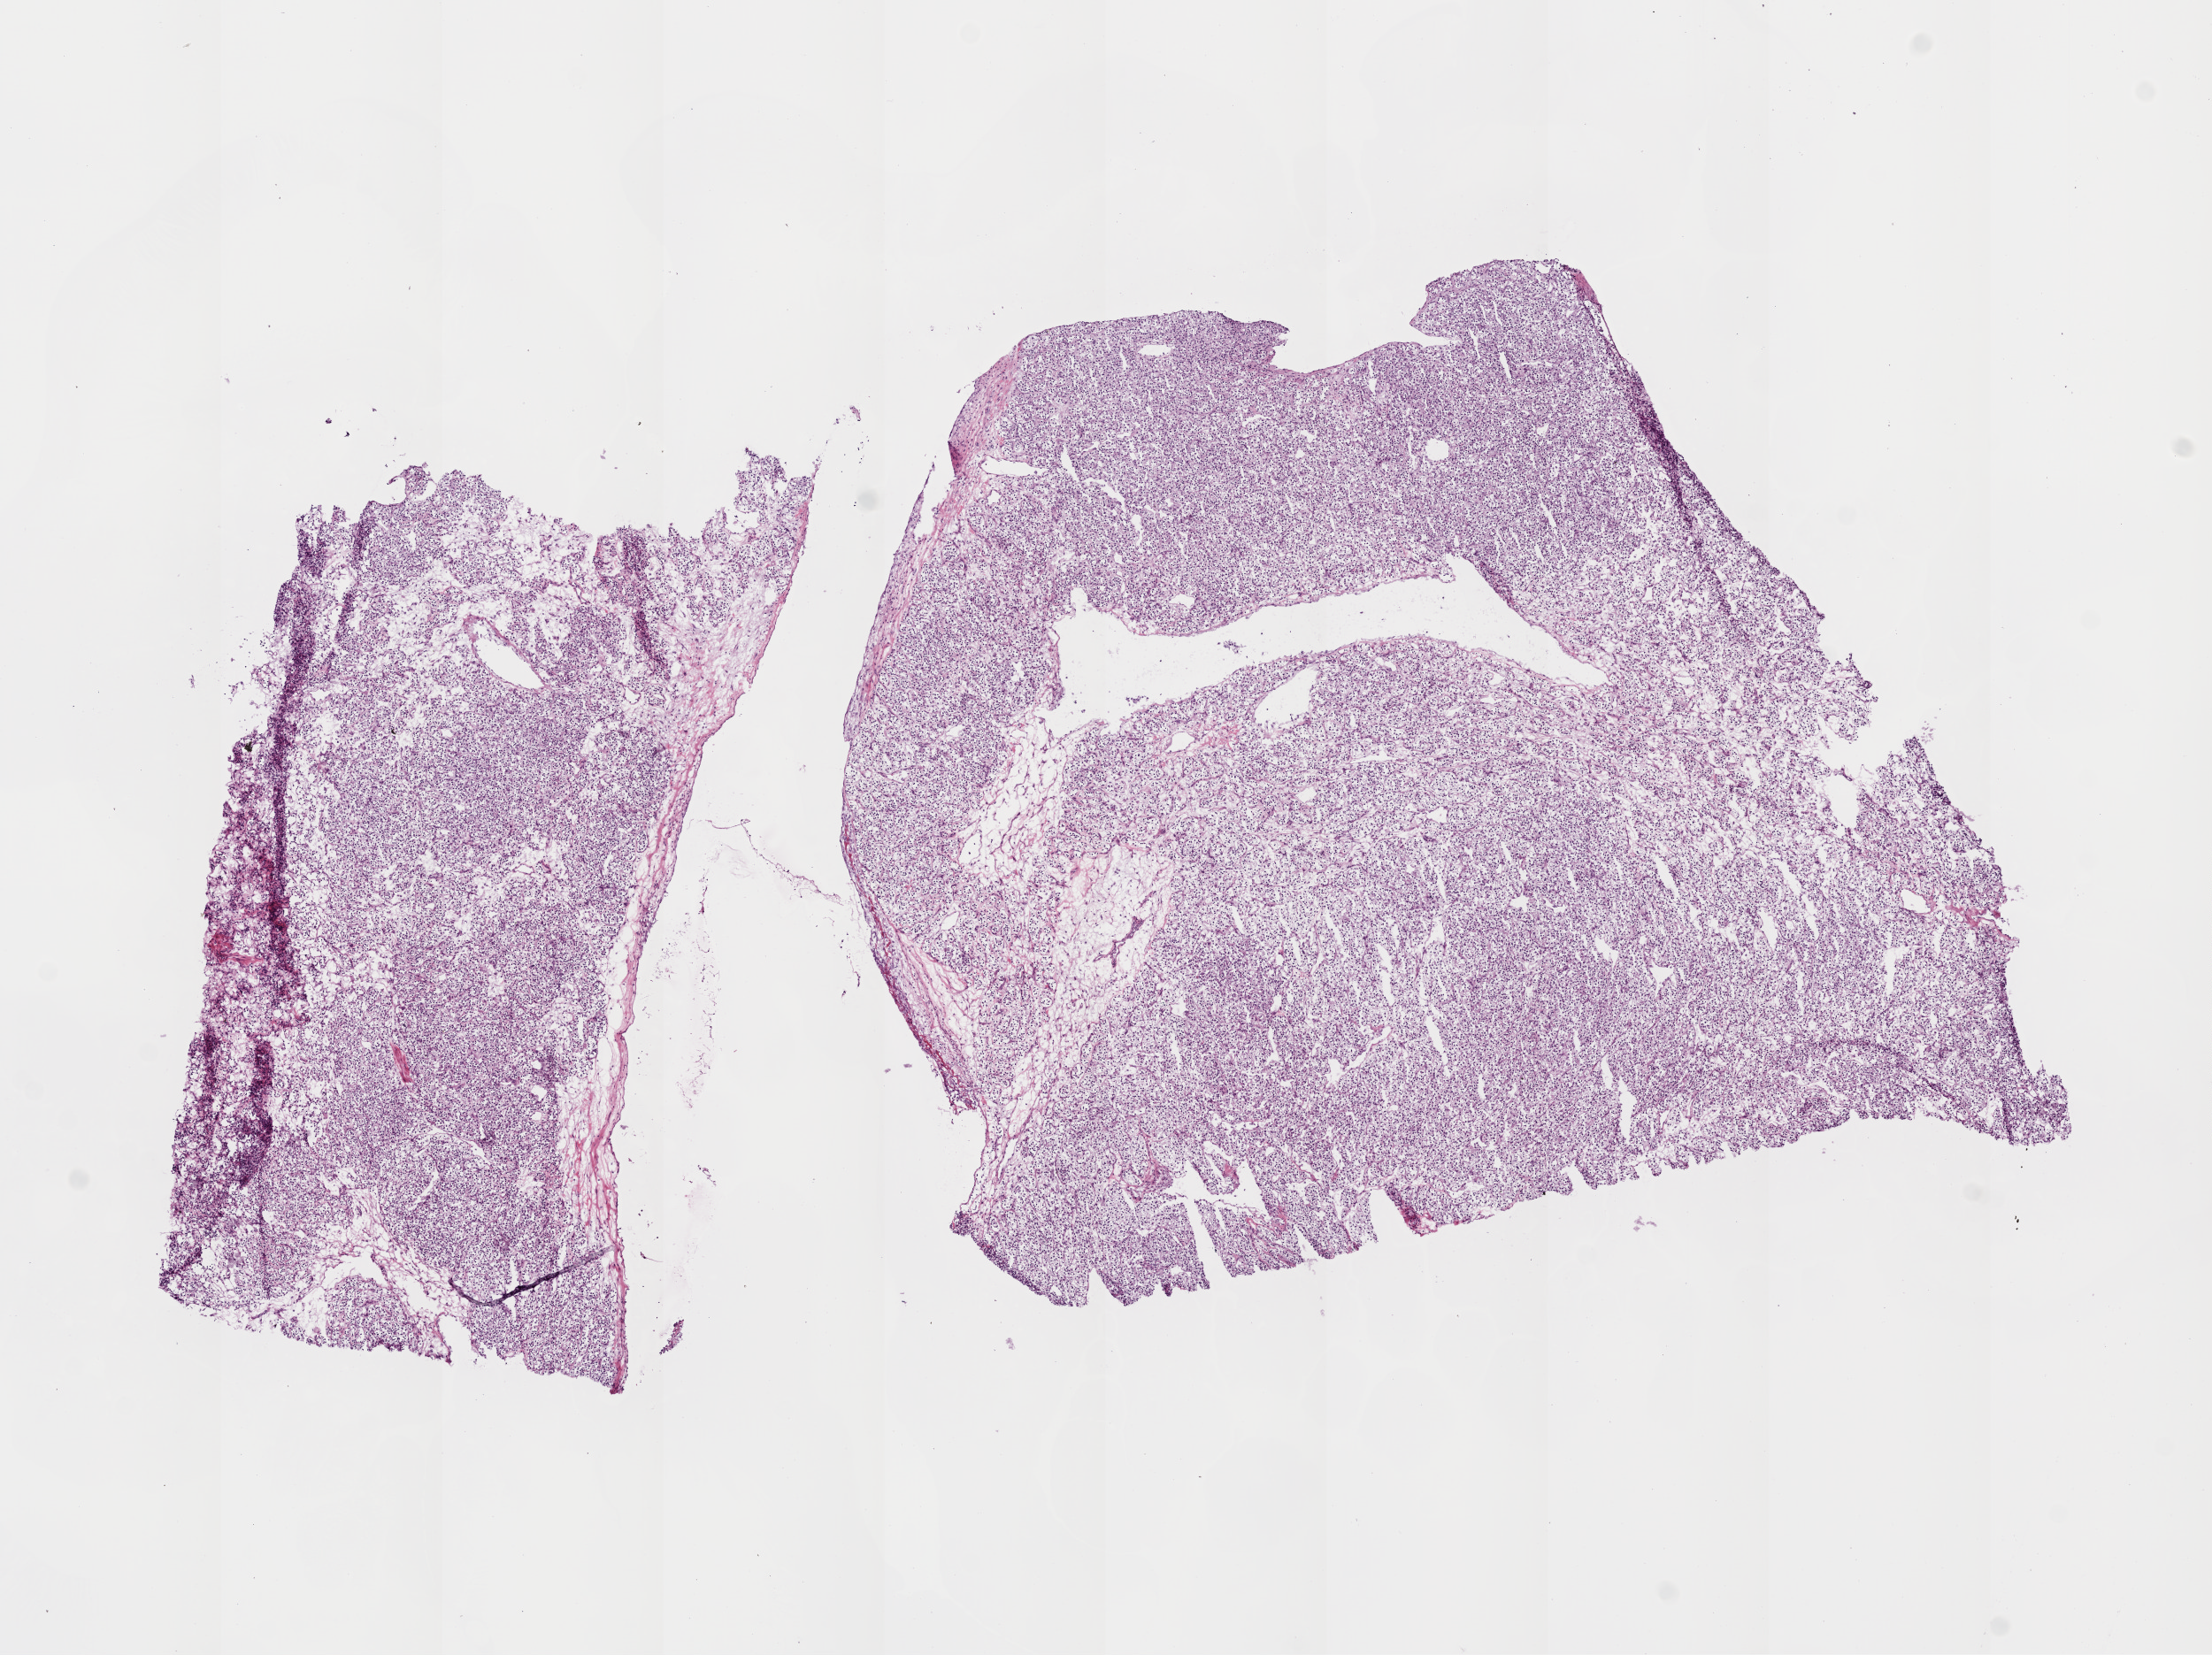
Digitized H&E-stained tissue section (whole slide) — whole scanned area (about 10.0 x 7.5 mm, acquisition: 20x scan) shown as a low-resolution overview. Frozen section. Kidney, primary tumour sample. Male, age 51 years at initial diagnosis. Histologic grade: G2 (moderately differentiated). Pathologist review of this section (percent, as recorded): tumour cells 90%, tumour nuclei 85%, normal cells 0%, stromal cells 10%, necrosis 0%.
AJCC pathologic stage: IV. Diagnosis: Clear cell adenocarcinoma, NOS. Laterality: right. Lymph nodes positive (case pathology): 0 of 17 examined.